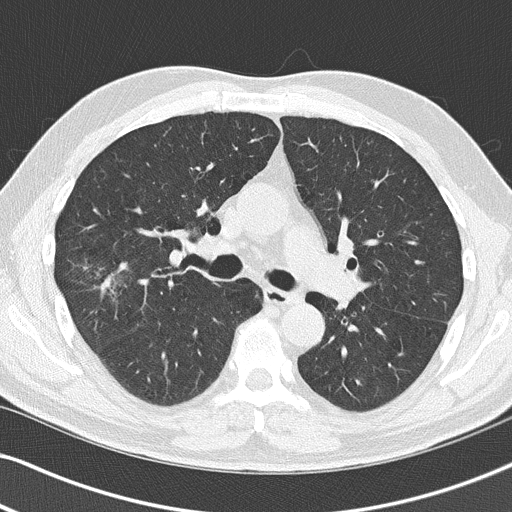
Low-dose screening chest CT, one axial slice. Slice 79 of 140 in the series (ordered by position). Reconstruction kernel B50f. 120 kVp. Lung window (W 1500 / L -600 HU). 2 mm slice thickness. 512 × 512 image matrix, field of view 330 × 330 mm.
Outlined on this slice (expert manual segmentation):
- lesion 1 (tumor, upper lobe of right lung): bounding box [x1, y1, x2, y2] px = [104, 263, 128, 289]